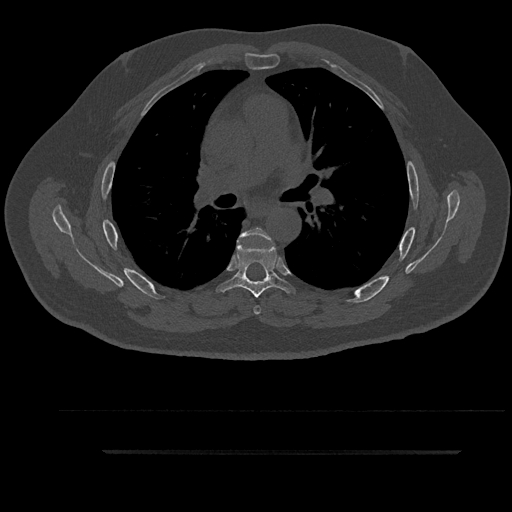
CT including the spine, one axial slice; 120 kVp; bone window (W 1800 / L 400 HU); 0.5 mm slice thickness; 512 × 512 image matrix, field of view 432 × 432 mm. Male patient, age 63 years. From the clinical record (not read from this slice): primary cancer: renal; vertebrae with lytic lesions (as recorded): T8.
Annotated regions visible in this slice (semi-automatic segmentation, software-assisted and operator-edited):
- T5 vertebra: bounding box (x1, y1, x2, y2) in pixels: (237, 227, 274, 315)
- T6 vertebra: (221, 237, 290, 298)